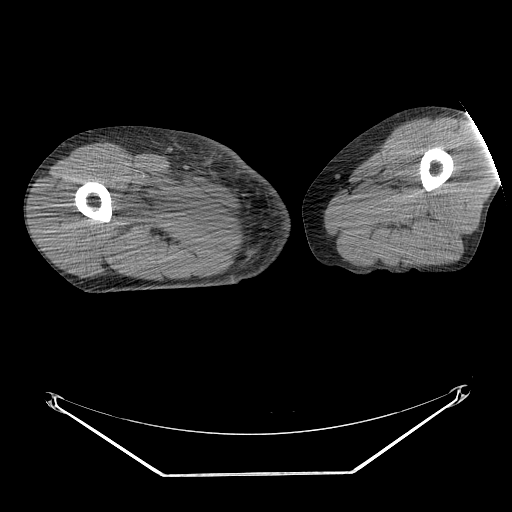
CT of an extremity soft-tissue mass (from a PET/CT study), one axial slice; position 238 of 311 along the scan axis; reconstruction kernel STANDARD; 140 kVp; soft-tissue window (W 400 / L 40 HU); 3.75 mm slice thickness; 512 × 512 image matrix, field of view 500 × 500 mm. Male patient. From the clinical record (not read from this slice): histological type: undifferentiated - pleiomorphic; grade: high; site of the primary tumour: right thigh.
Structures marked on this image (expert contour drawn on MRI and transferred to this co-registered scan by the dataset authors):
- gross tumour volume including surrounding oedema: bounding box [x1, y1, x2, y2] px = [130, 181, 207, 231]